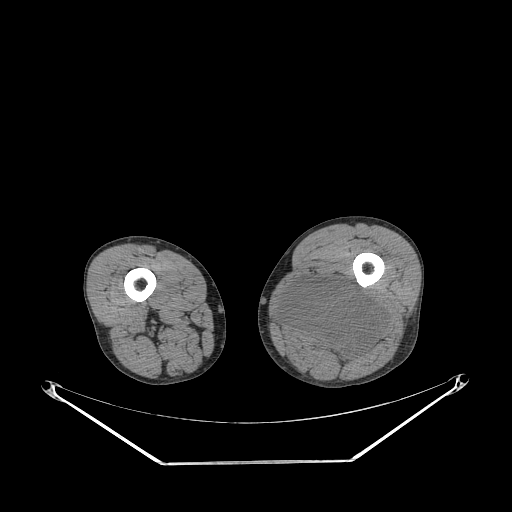
CT of an extremity soft-tissue mass (from a PET/CT study), one axial slice; slice 224 of 267 in the series (ordered by position); 140 kVp; soft-tissue window (W 400 / L 40 HU); 3.75 mm slice thickness; 512 × 512 image matrix, field of view 500 × 500 mm. Male patient. From the clinical record (not read from this slice): histological type: undifferentiated pleomorphic liposarcoma; grade: high; site of the primary tumour: left thigh.
Outlined on this slice (expert contour drawn on MRI and transferred to this co-registered scan by the dataset authors):
- gross tumour volume including surrounding oedema: bounding box [x1, y1, x2, y2] px = [279, 278, 385, 362]
- gross tumour volume (mass): [281, 278, 385, 362]